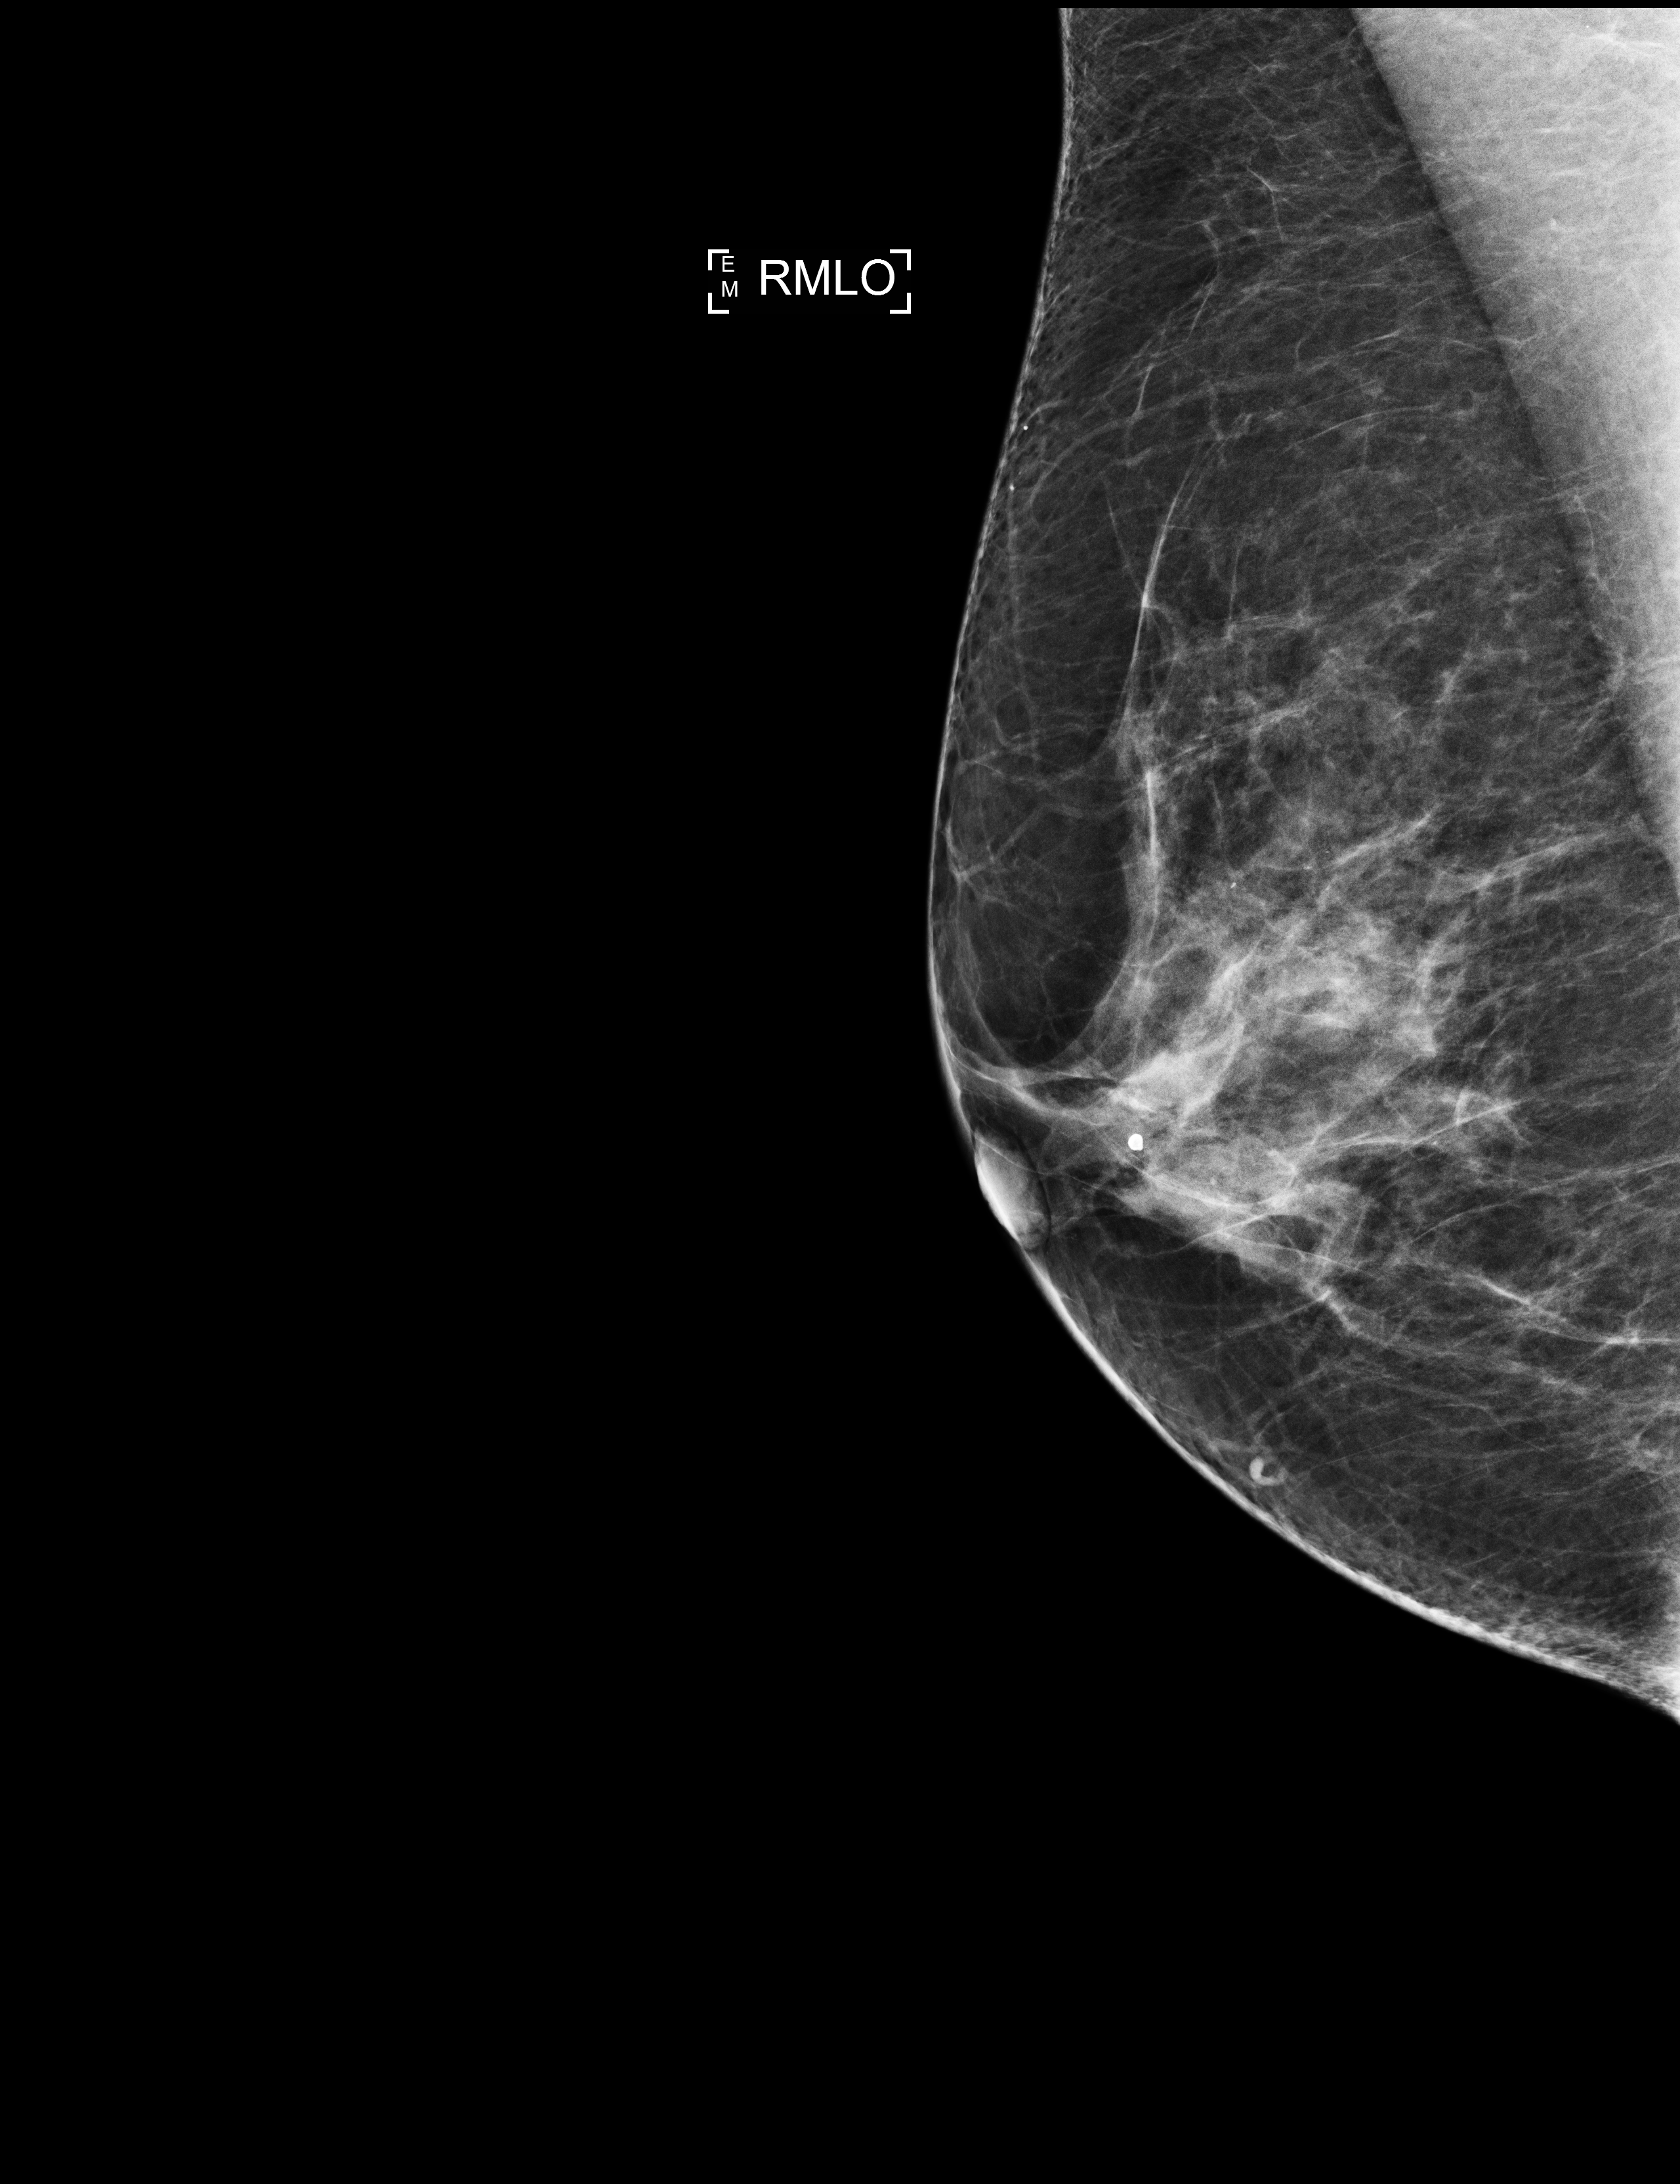
Annual screening mammography examination, compressed breast thickness 59 mm. Patient: female, 57 years.
Image type: full-field digital mammogram. Breast: right. Projection: MLO view.